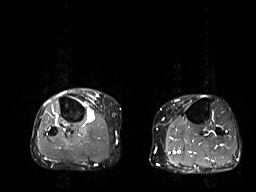
MRI of an extremity soft-tissue mass, one axial slice; position 20 of 32 along the scan axis; STIR; 6 mm slice thickness; 256 × 192 image matrix, field of view 375 × 281 mm. Female patient. Case-level facts recorded for this patient, not image findings: histological type: undifferentiated – high grade; grade: high; site of the primary tumour: right thigh.
Structures marked on this image (outlined manually by an expert reader):
- gross tumour volume (mass): bounding box <84,110,95,122> (left, top, right, bottom; pixels)